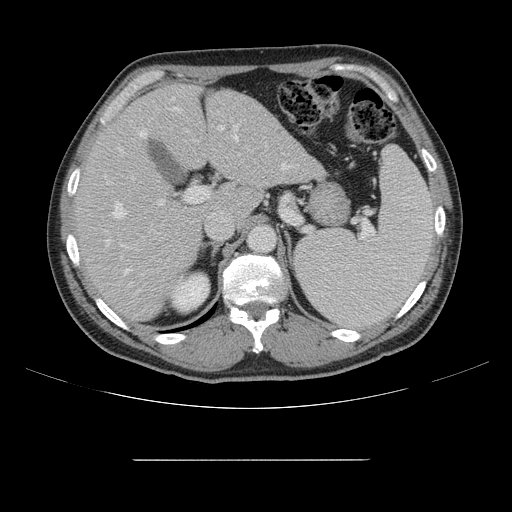
Contrast-enhanced abdominal CT, one axial slice. Slice 99 of 164 in the series (ordered by position). 120 kVp. Soft-tissue window (W 400 / L 40 HU). 2.5 mm slice thickness. 512 × 512 image matrix, field of view 404 × 404 mm. Male patient, age 54 years. Case-level facts recorded for this patient, not image findings: diagnosis: colorectal cancer liver metastases, imaged before liver resection; multiple liver metastases: yes; largest metastasis: 1 cm; disease in both lobes: no.
Outlined on this slice (outlined manually by an expert reader):
- hepatic veins: box from (x=106, y=133) to (x=292, y=275) px
- liver: (x=77, y=85)–(x=321, y=322)
- planned liver remnant (the part of the liver to remain after resection): (x=77, y=85)–(x=236, y=321)
- portal vein (with intrahepatic branches): (x=118, y=97)–(x=240, y=296)